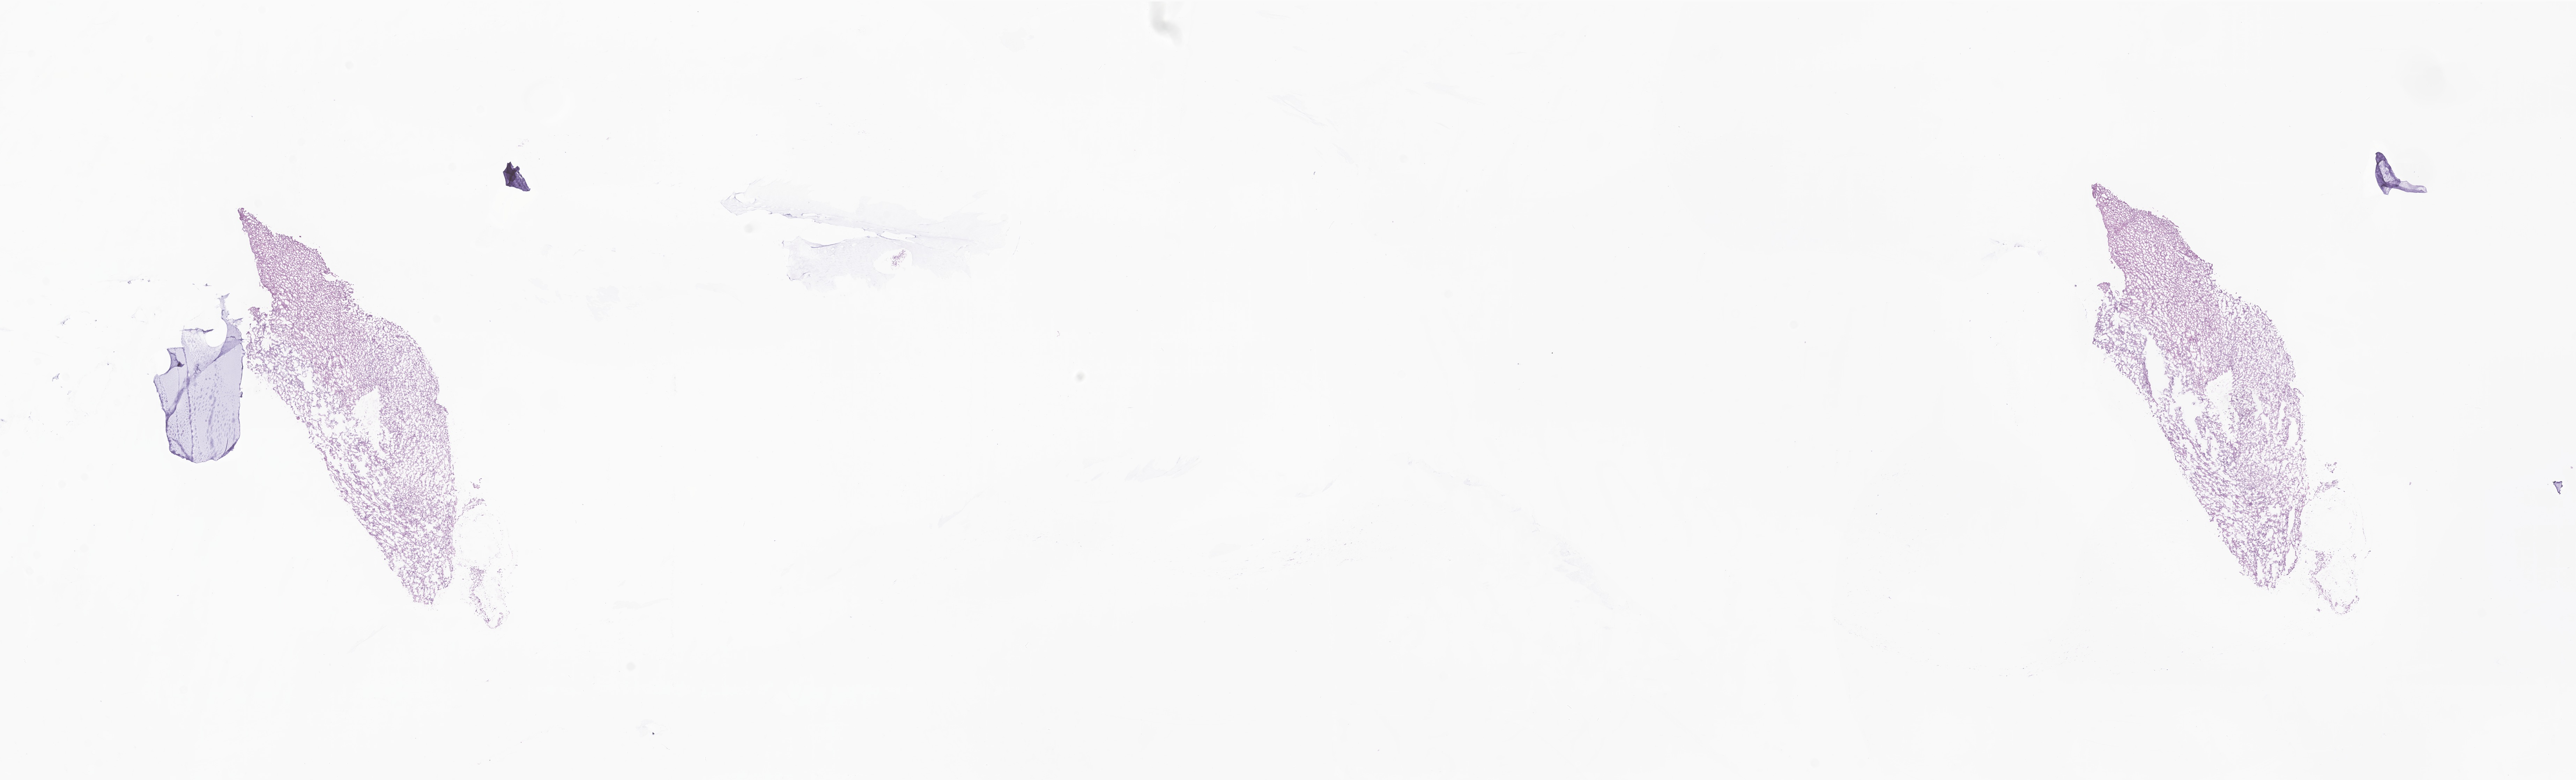
Whole-slide image, H&E stain of tumor tissue from the brain — whole scanned area (about 31.1 x 9.4 mm) shown as a low-resolution overview. Cryosection (OCT / tissue freezing medium). Patient female; age 135 months (11 years 3 months).
Recorded diagnosis: Ganglioglioma, NOS.